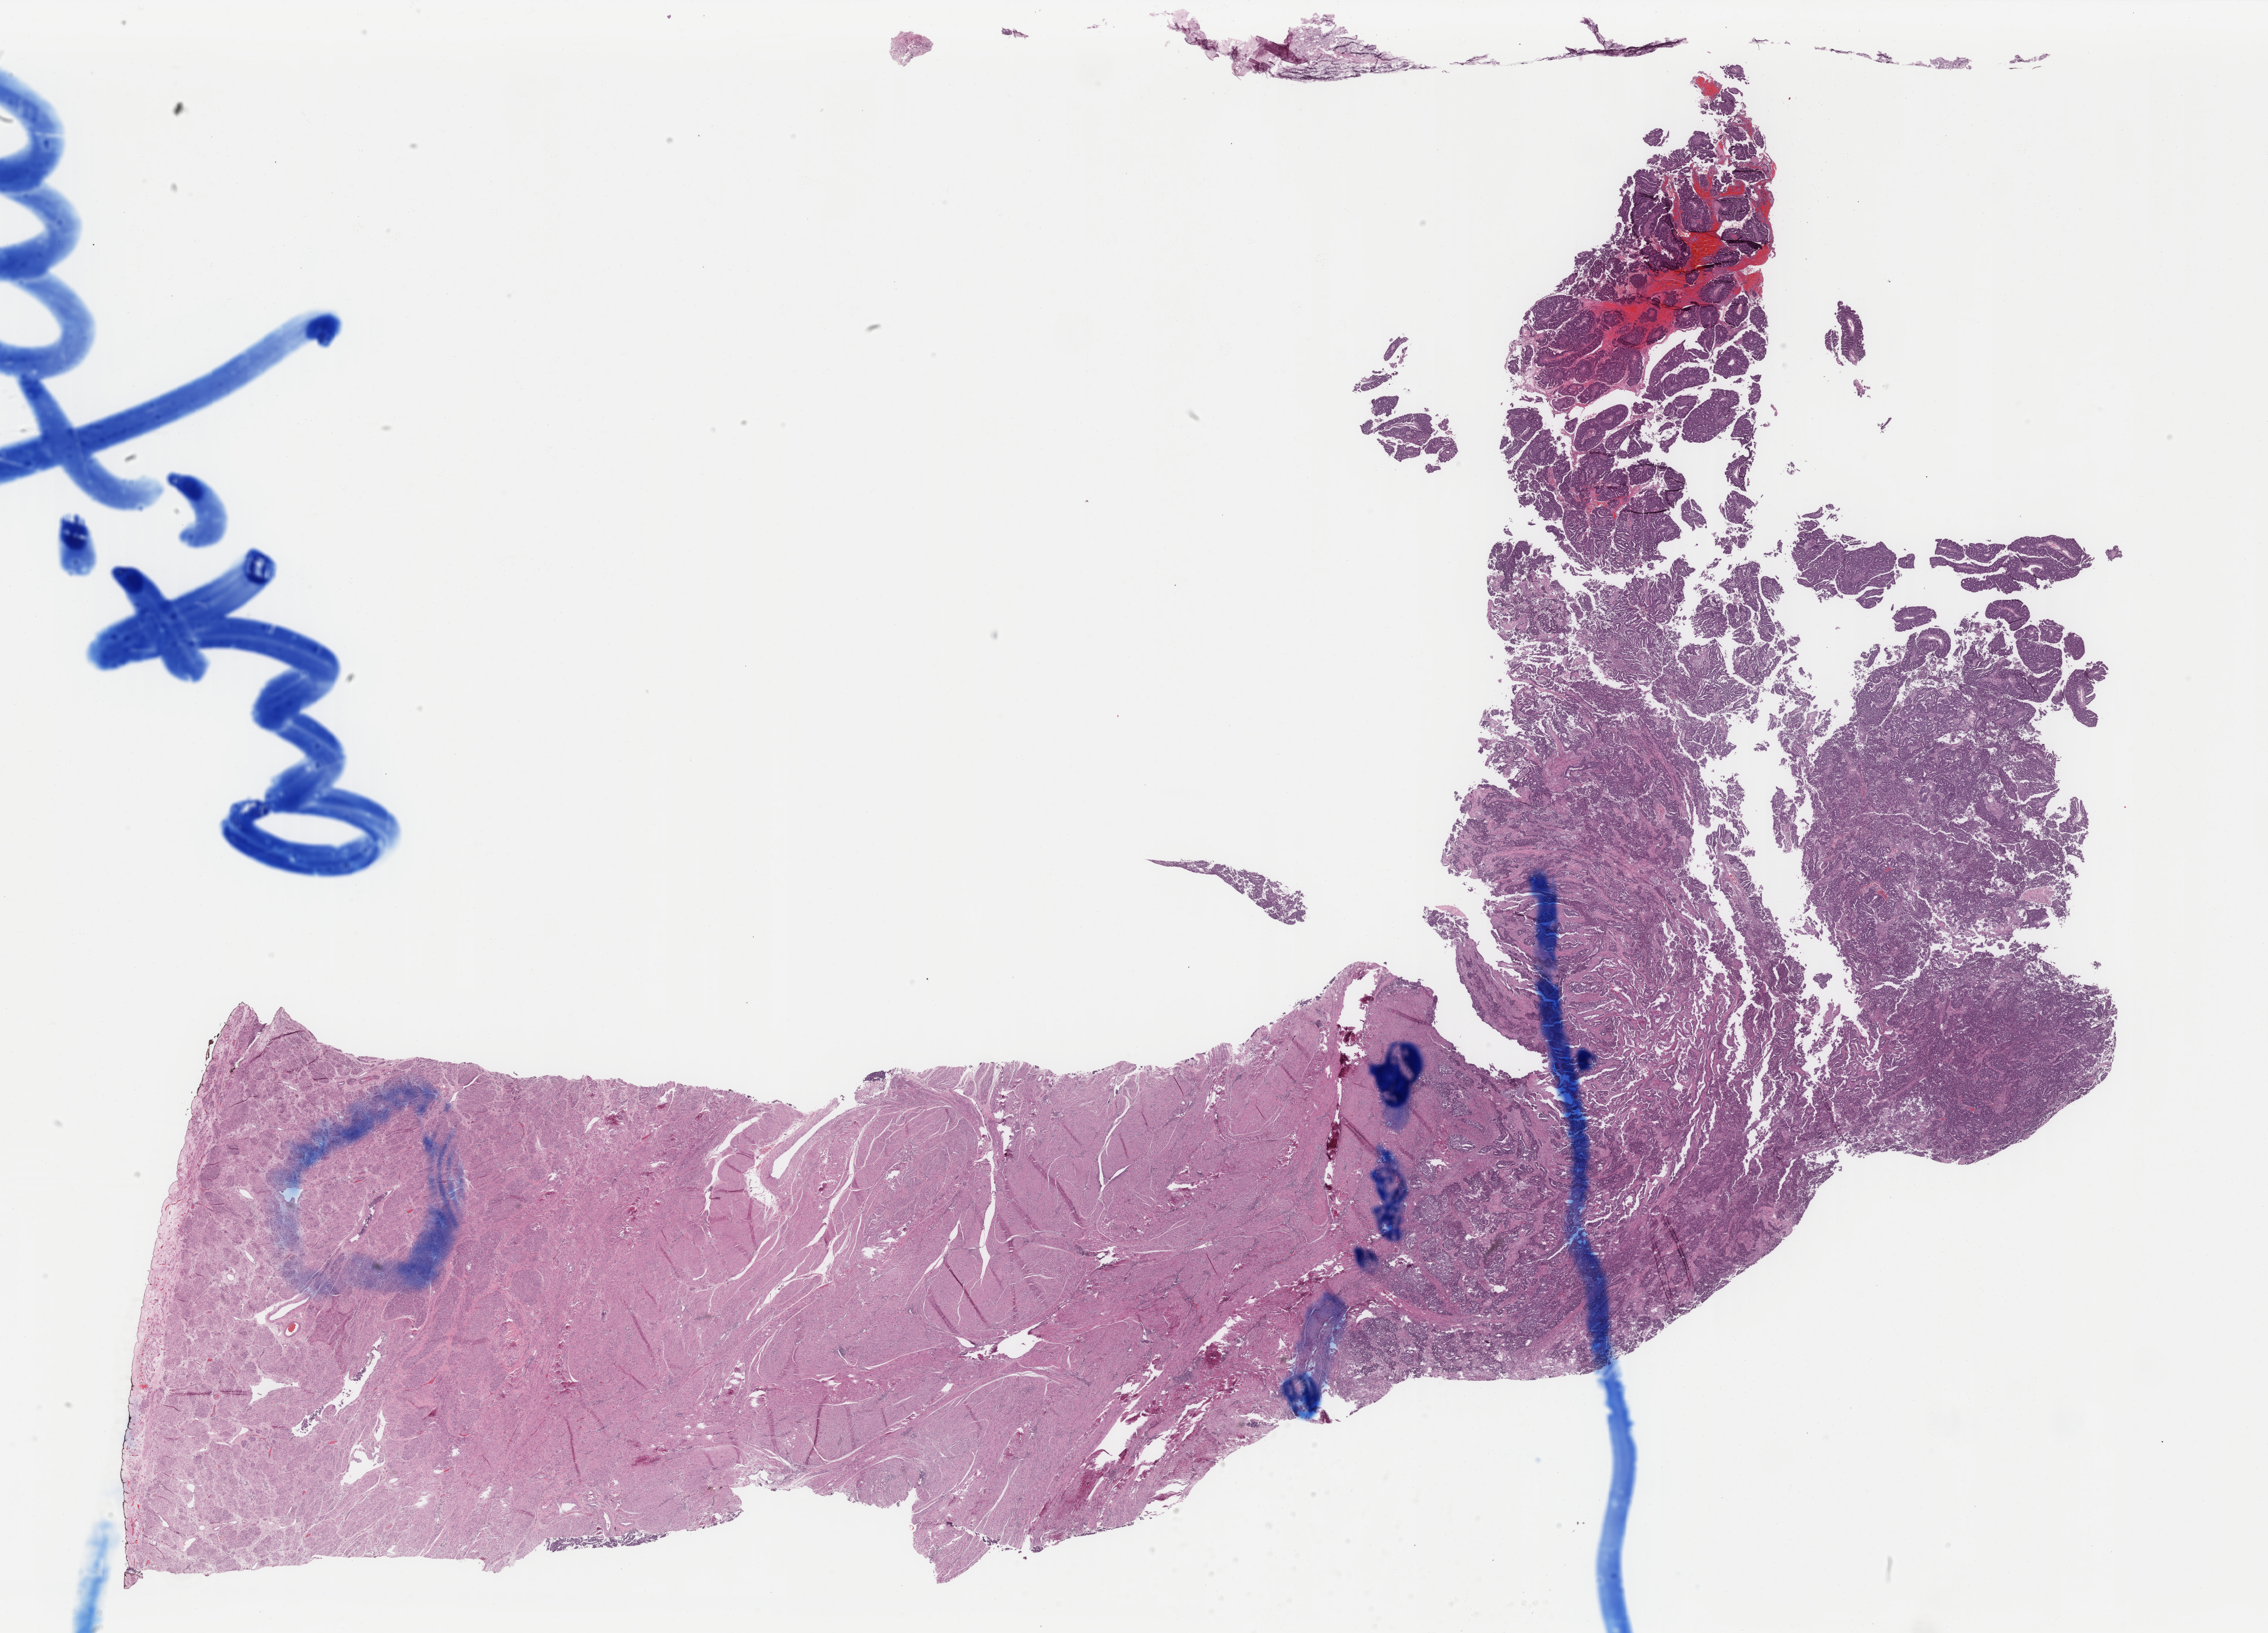
H&E-stained whole-slide image — a low-resolution overview of the entire scanned area, about 30.7 x 22.1 mm (acquisition: 40x scan), formalin-fixed paraffin-embedded (FFPE) diagnostic section, primary tumour sample from the uterus. Female, age 52 years at initial diagnosis. Histologic grade: G2 (moderately differentiated).
• FIGO stage: IB
• diagnosis: Endometrioid adenocarcinoma, NOS (endometrium)